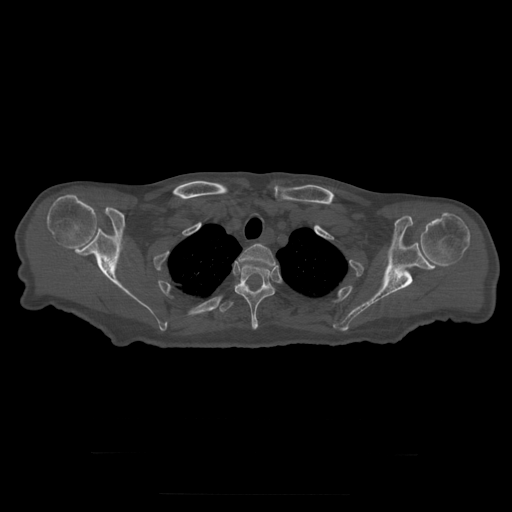
CT including the spine, one axial slice; slice 259 of 397 in the series (ordered by position); reconstruction kernel STANDARD; bone window (W 1800 / L 400 HU); 512 × 512 image matrix, field of view 510 × 510 mm. Patient age 73 years. Case-level facts recorded for this patient, not image findings: primary cancer: prostate.
Outlined on this slice (semi-automatically segmented with operator editing):
- T2 vertebra: bounding box [x1, y1, x2, y2] px = [239, 244, 277, 269]
- T3 vertebra: [235, 264, 275, 330]
- T4 vertebra: [219, 284, 264, 313]